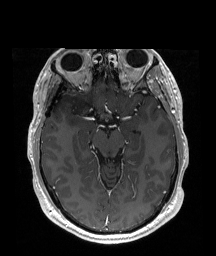
Brain MRI from a brain-tumour surgery series, one axial slice; T1-weighted post-contrast; 216 × 256 image matrix, field of view 219 × 260 mm. From the clinical record (not read from this slice): histopathology: Astrocytoma; WHO grade: 2; IDH mutation: yes; tumour location: Right Insular.
Annotated regions visible in this slice (manually delineated by an expert):
- tumour: bounding box (x1, y1, x2, y2) in pixels: (67, 95, 91, 127)